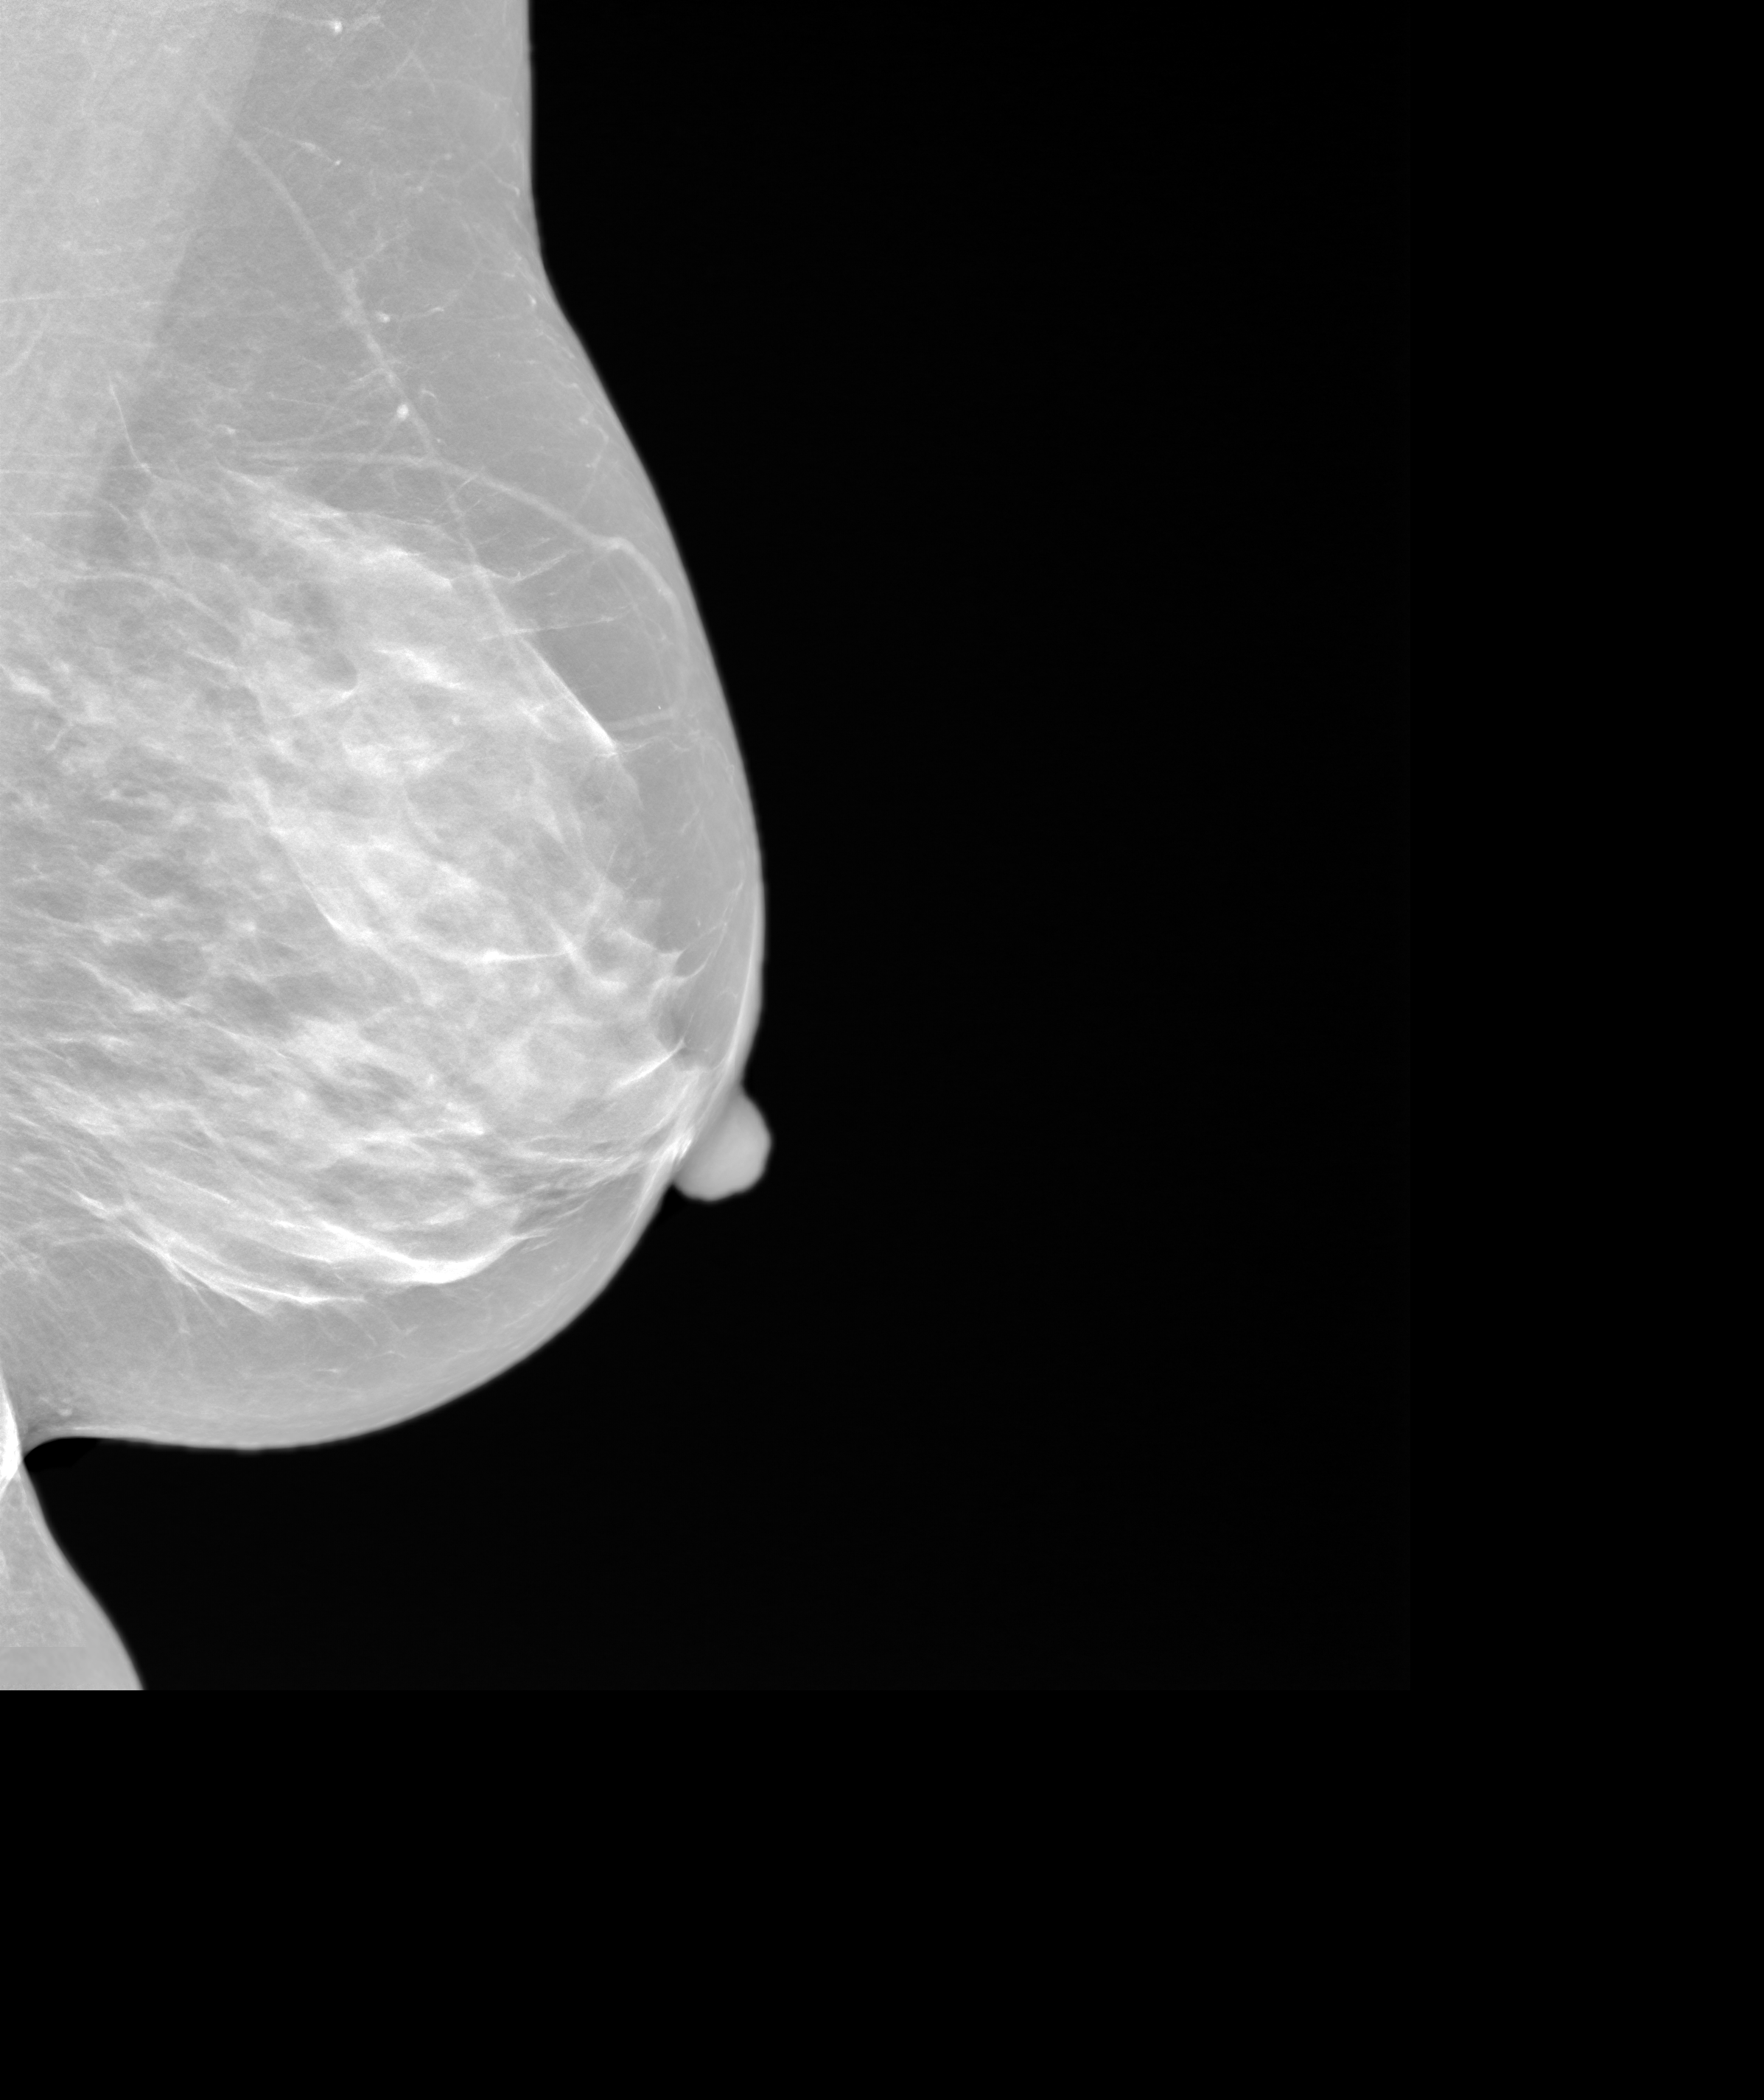
Annual screening mammography examination, system: SenoIris_1SP2(440). Patient aged 68 years (female).
Image type: synthesized 2-D view from tomosynthesis. Breast: left. Projection: medio-lateral oblique projection.